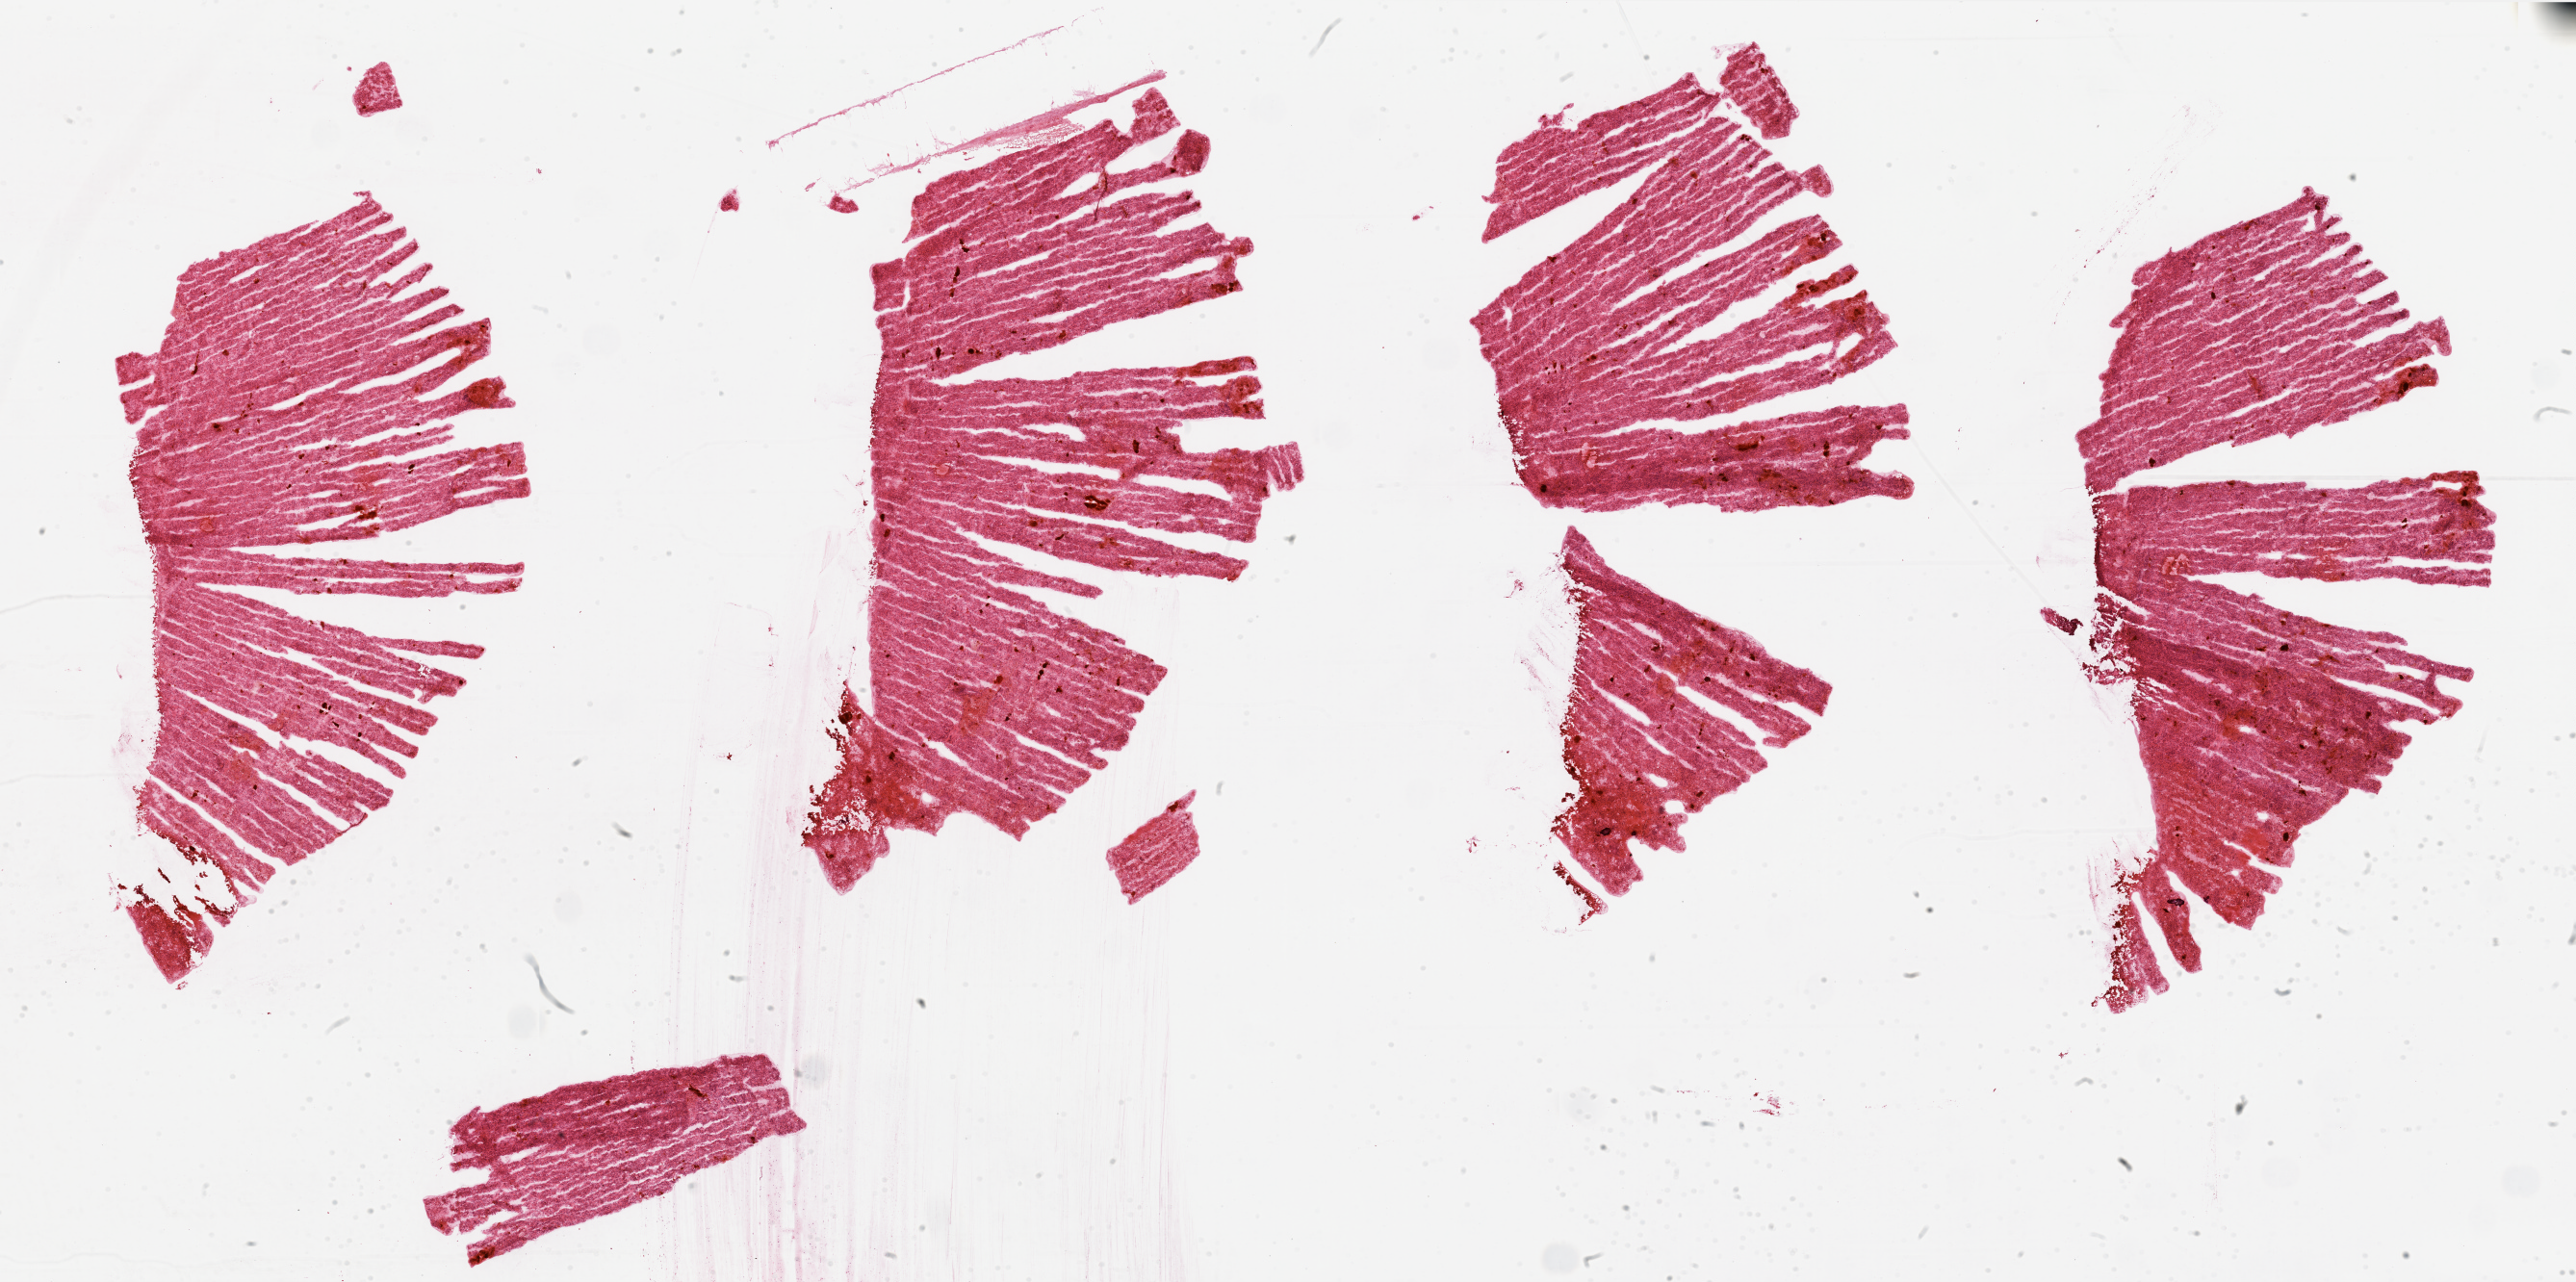
Digitized H&E tissue section (whole slide), shown as a low-resolution overview of the whole scanned area (about 42.3 x 21.1 mm, from a 20x scan), tumour tissue sample, sampled site: kidney. Female, 49 y/o. Histologic grade: G3 (poorly differentiated). Composition of this section per pathologist review: tumour nuclei 85%, necrosis 15%.
Diagnosis: Renal cell carcinoma, NOS. AJCC pathologic stage: II.